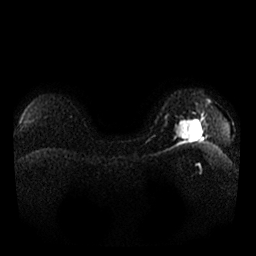
Breast MRI, one axial slice; slice 18 of 25 in the series (ordered by position); diffusion-weighted series; image 2 of 4 stored at this slice position (different b-values; order by instance number); 1.5 T; 4 mm slice thickness; 256 × 256 image matrix, field of view 340 × 340 mm. Female patient.
Outlined on this slice (outlined manually by an expert reader):
- tumour on diffusion-weighted imaging: box from (x=174, y=118) to (x=202, y=142) px